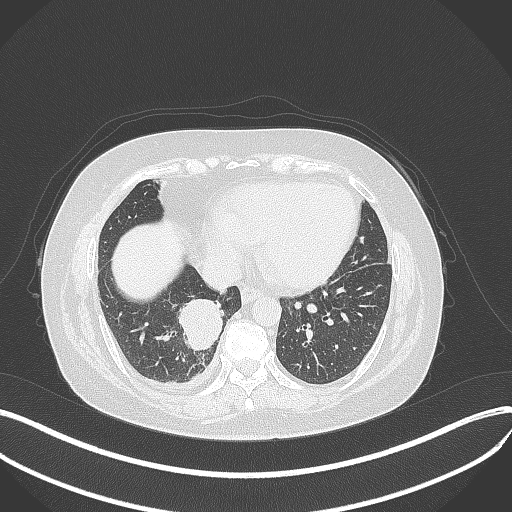
Chest CT, one axial slice. Position 118 of 381 along the scan axis. Lung window (W 1500 / L -600 HU). 1 mm slice thickness. 512 × 512 image matrix, field of view 400 × 400 mm. Patient: female, 56 years. From the clinical record (not read from this slice): clinical TNM (as recorded): T2b N1 M0; histopathological grade: G3.
Structures marked on this image (rectangle marked by the reading radiologist):
- lung tumour (recorded histology: small cell carcinoma): bounding box <176,297,225,354> (left, top, right, bottom; pixels)